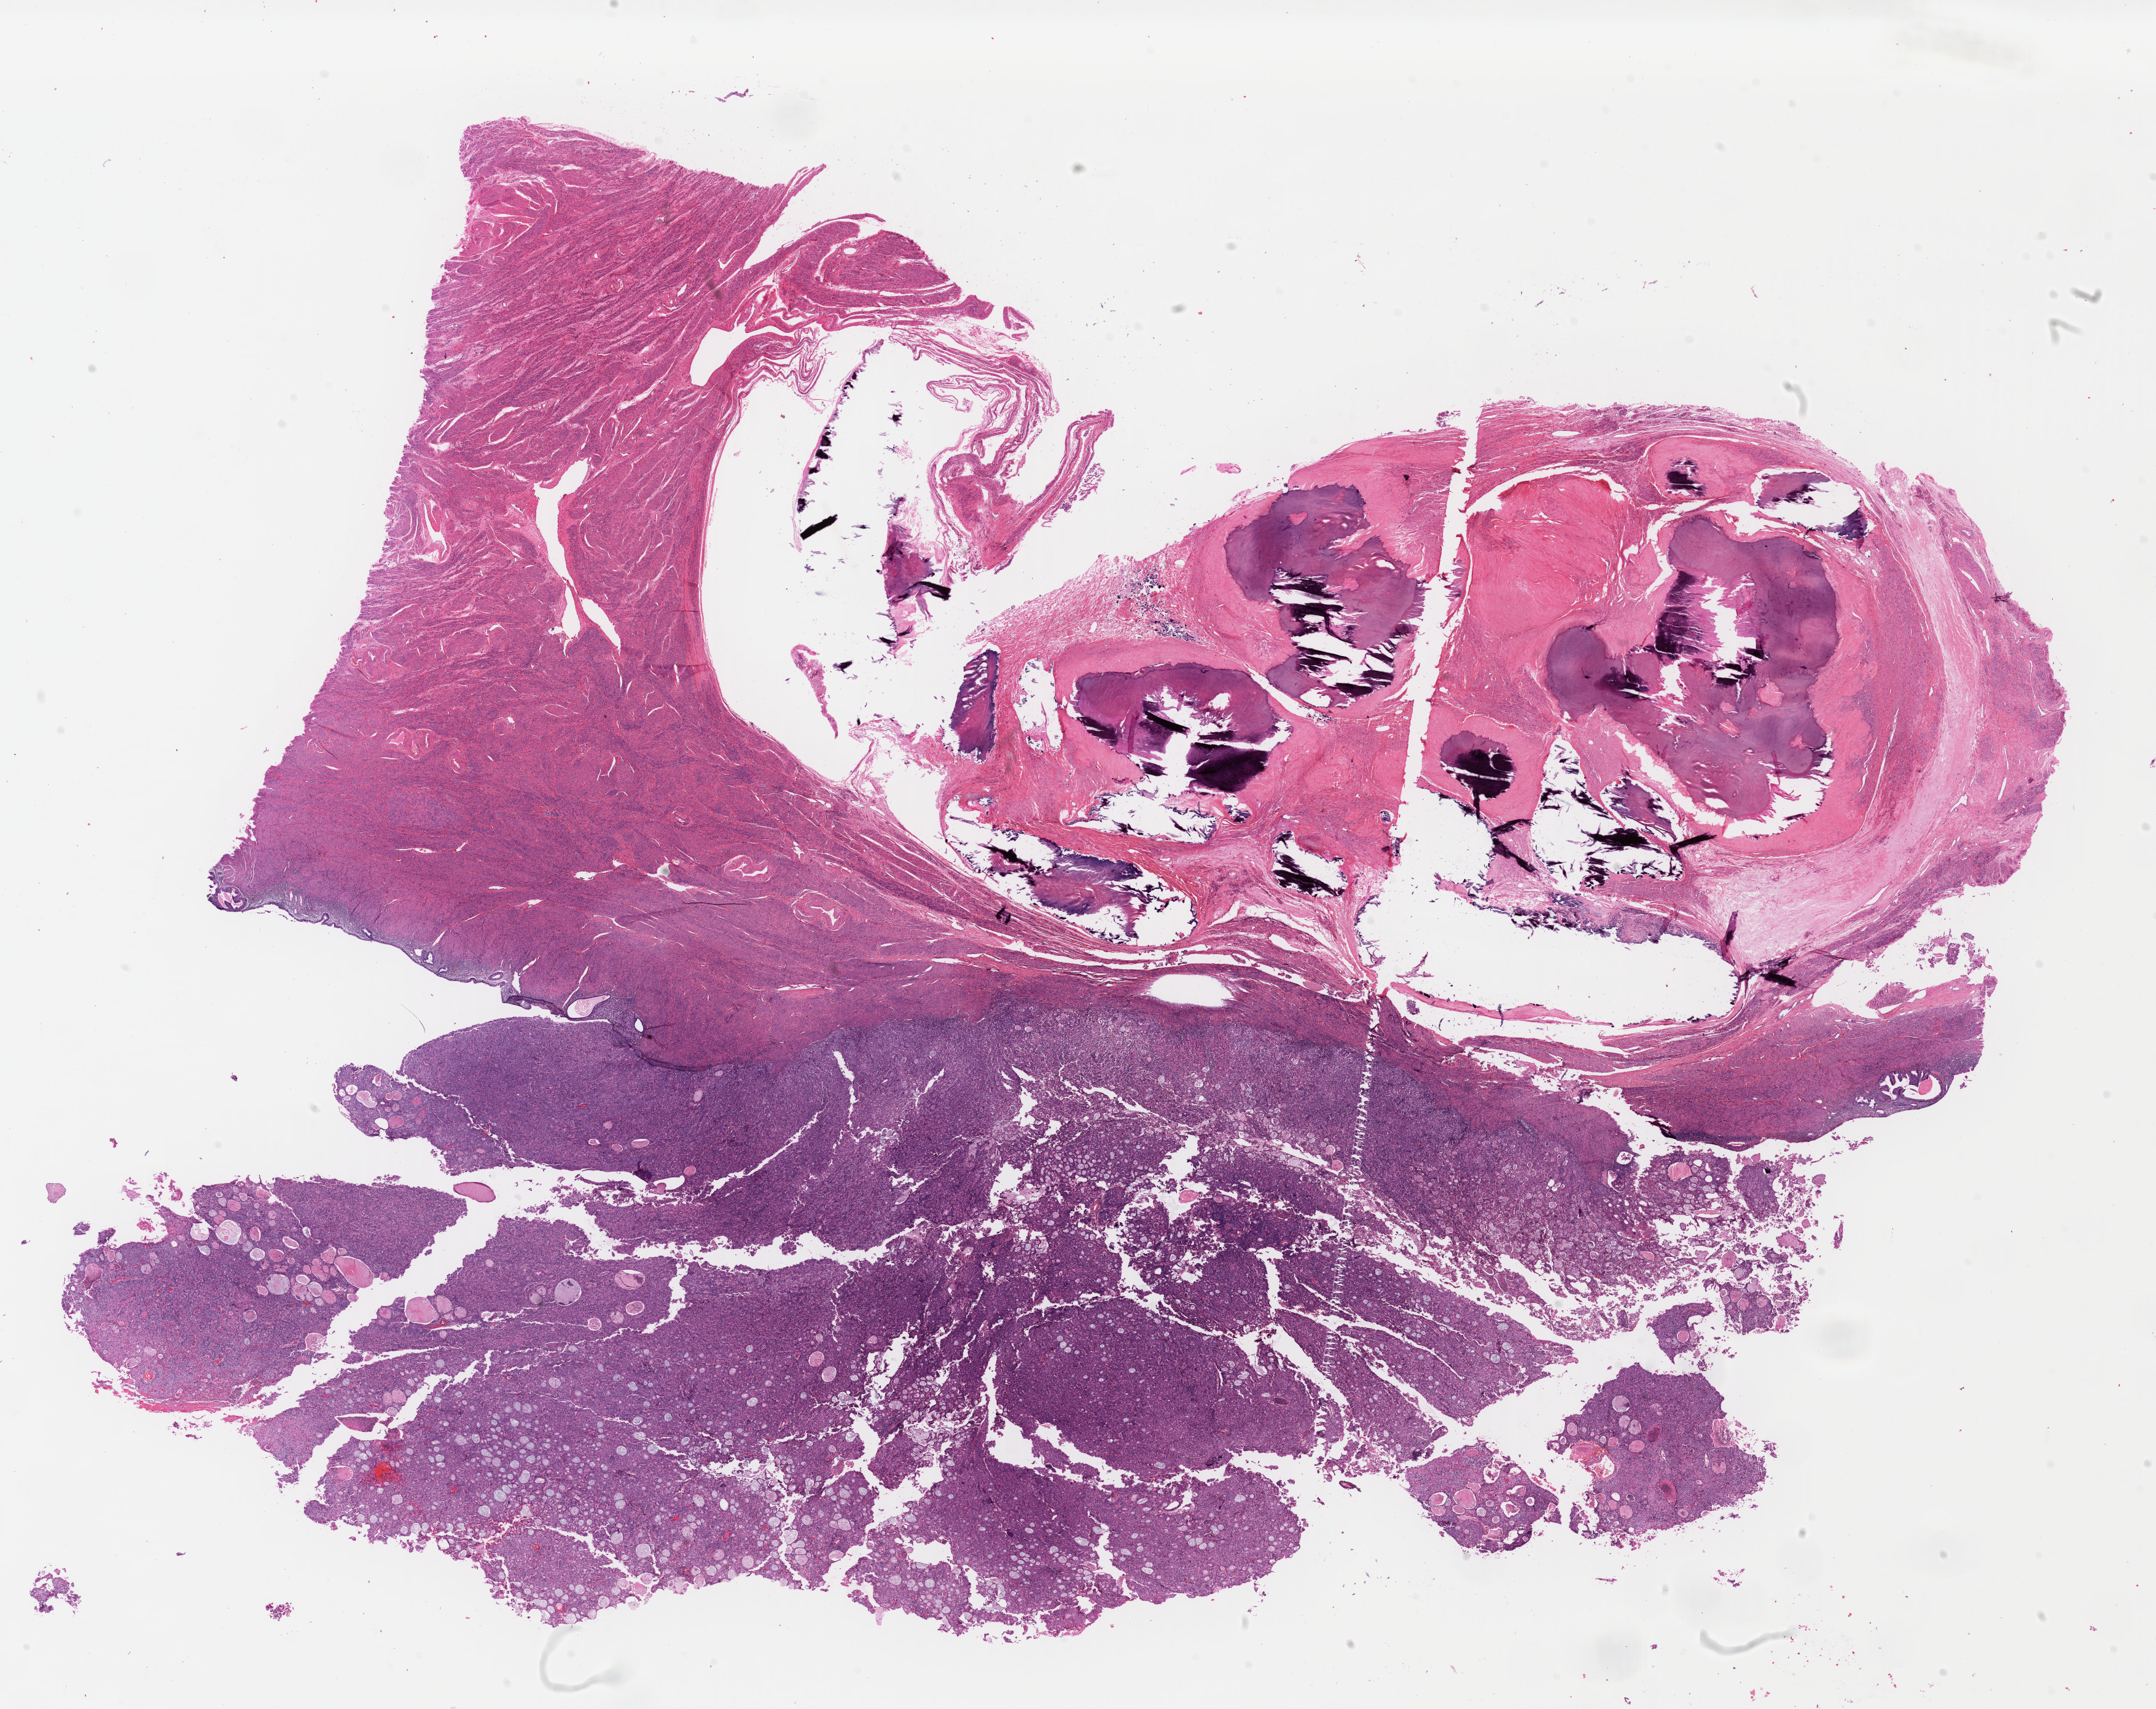
Whole-slide histology image, Hematoxylin and eosin (H&E) stained, shown as a low-resolution overview of the whole scanned area (about 27.6 x 21.9 mm, slide scanned at 40x). FFPE section. Primary tumour sample from the uterus. Female, age 74 years at initial diagnosis. Histologic grade: G3 (poorly differentiated).
FIGO stage: IA. Histologic diagnosis: Endometrioid adenocarcinoma, NOS.